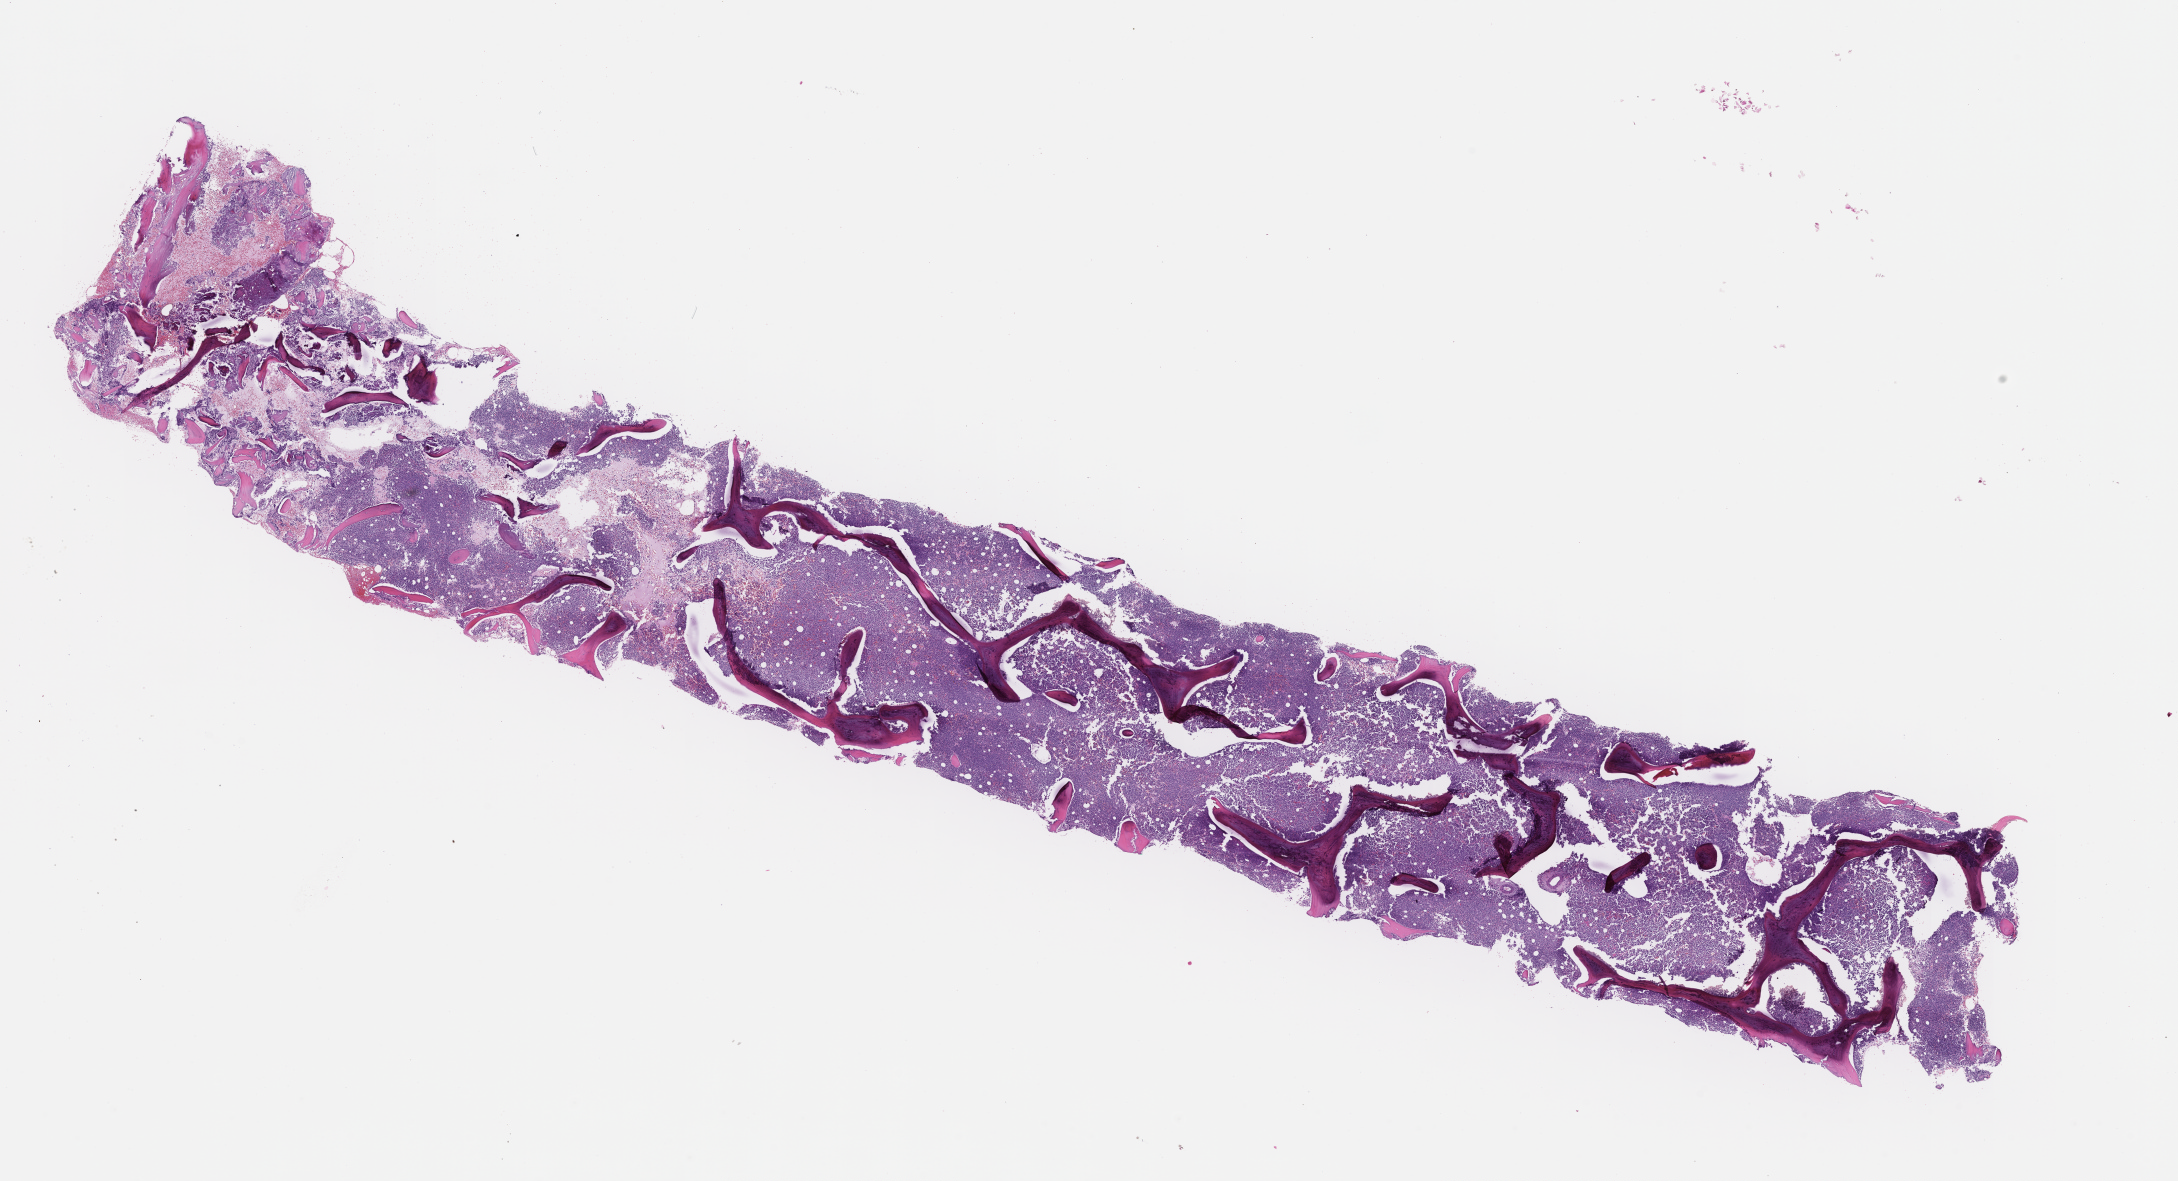
Hematoxylin and eosin (H&E) whole-slide image — low-resolution overview of the scanned area, about 17.6 x 9.5 mm. FFPE section. Tissue site: bone marrow. Patient sex: male.
- this section: primary tumour tissue
- diagnosis: Plasma Cell Myeloma